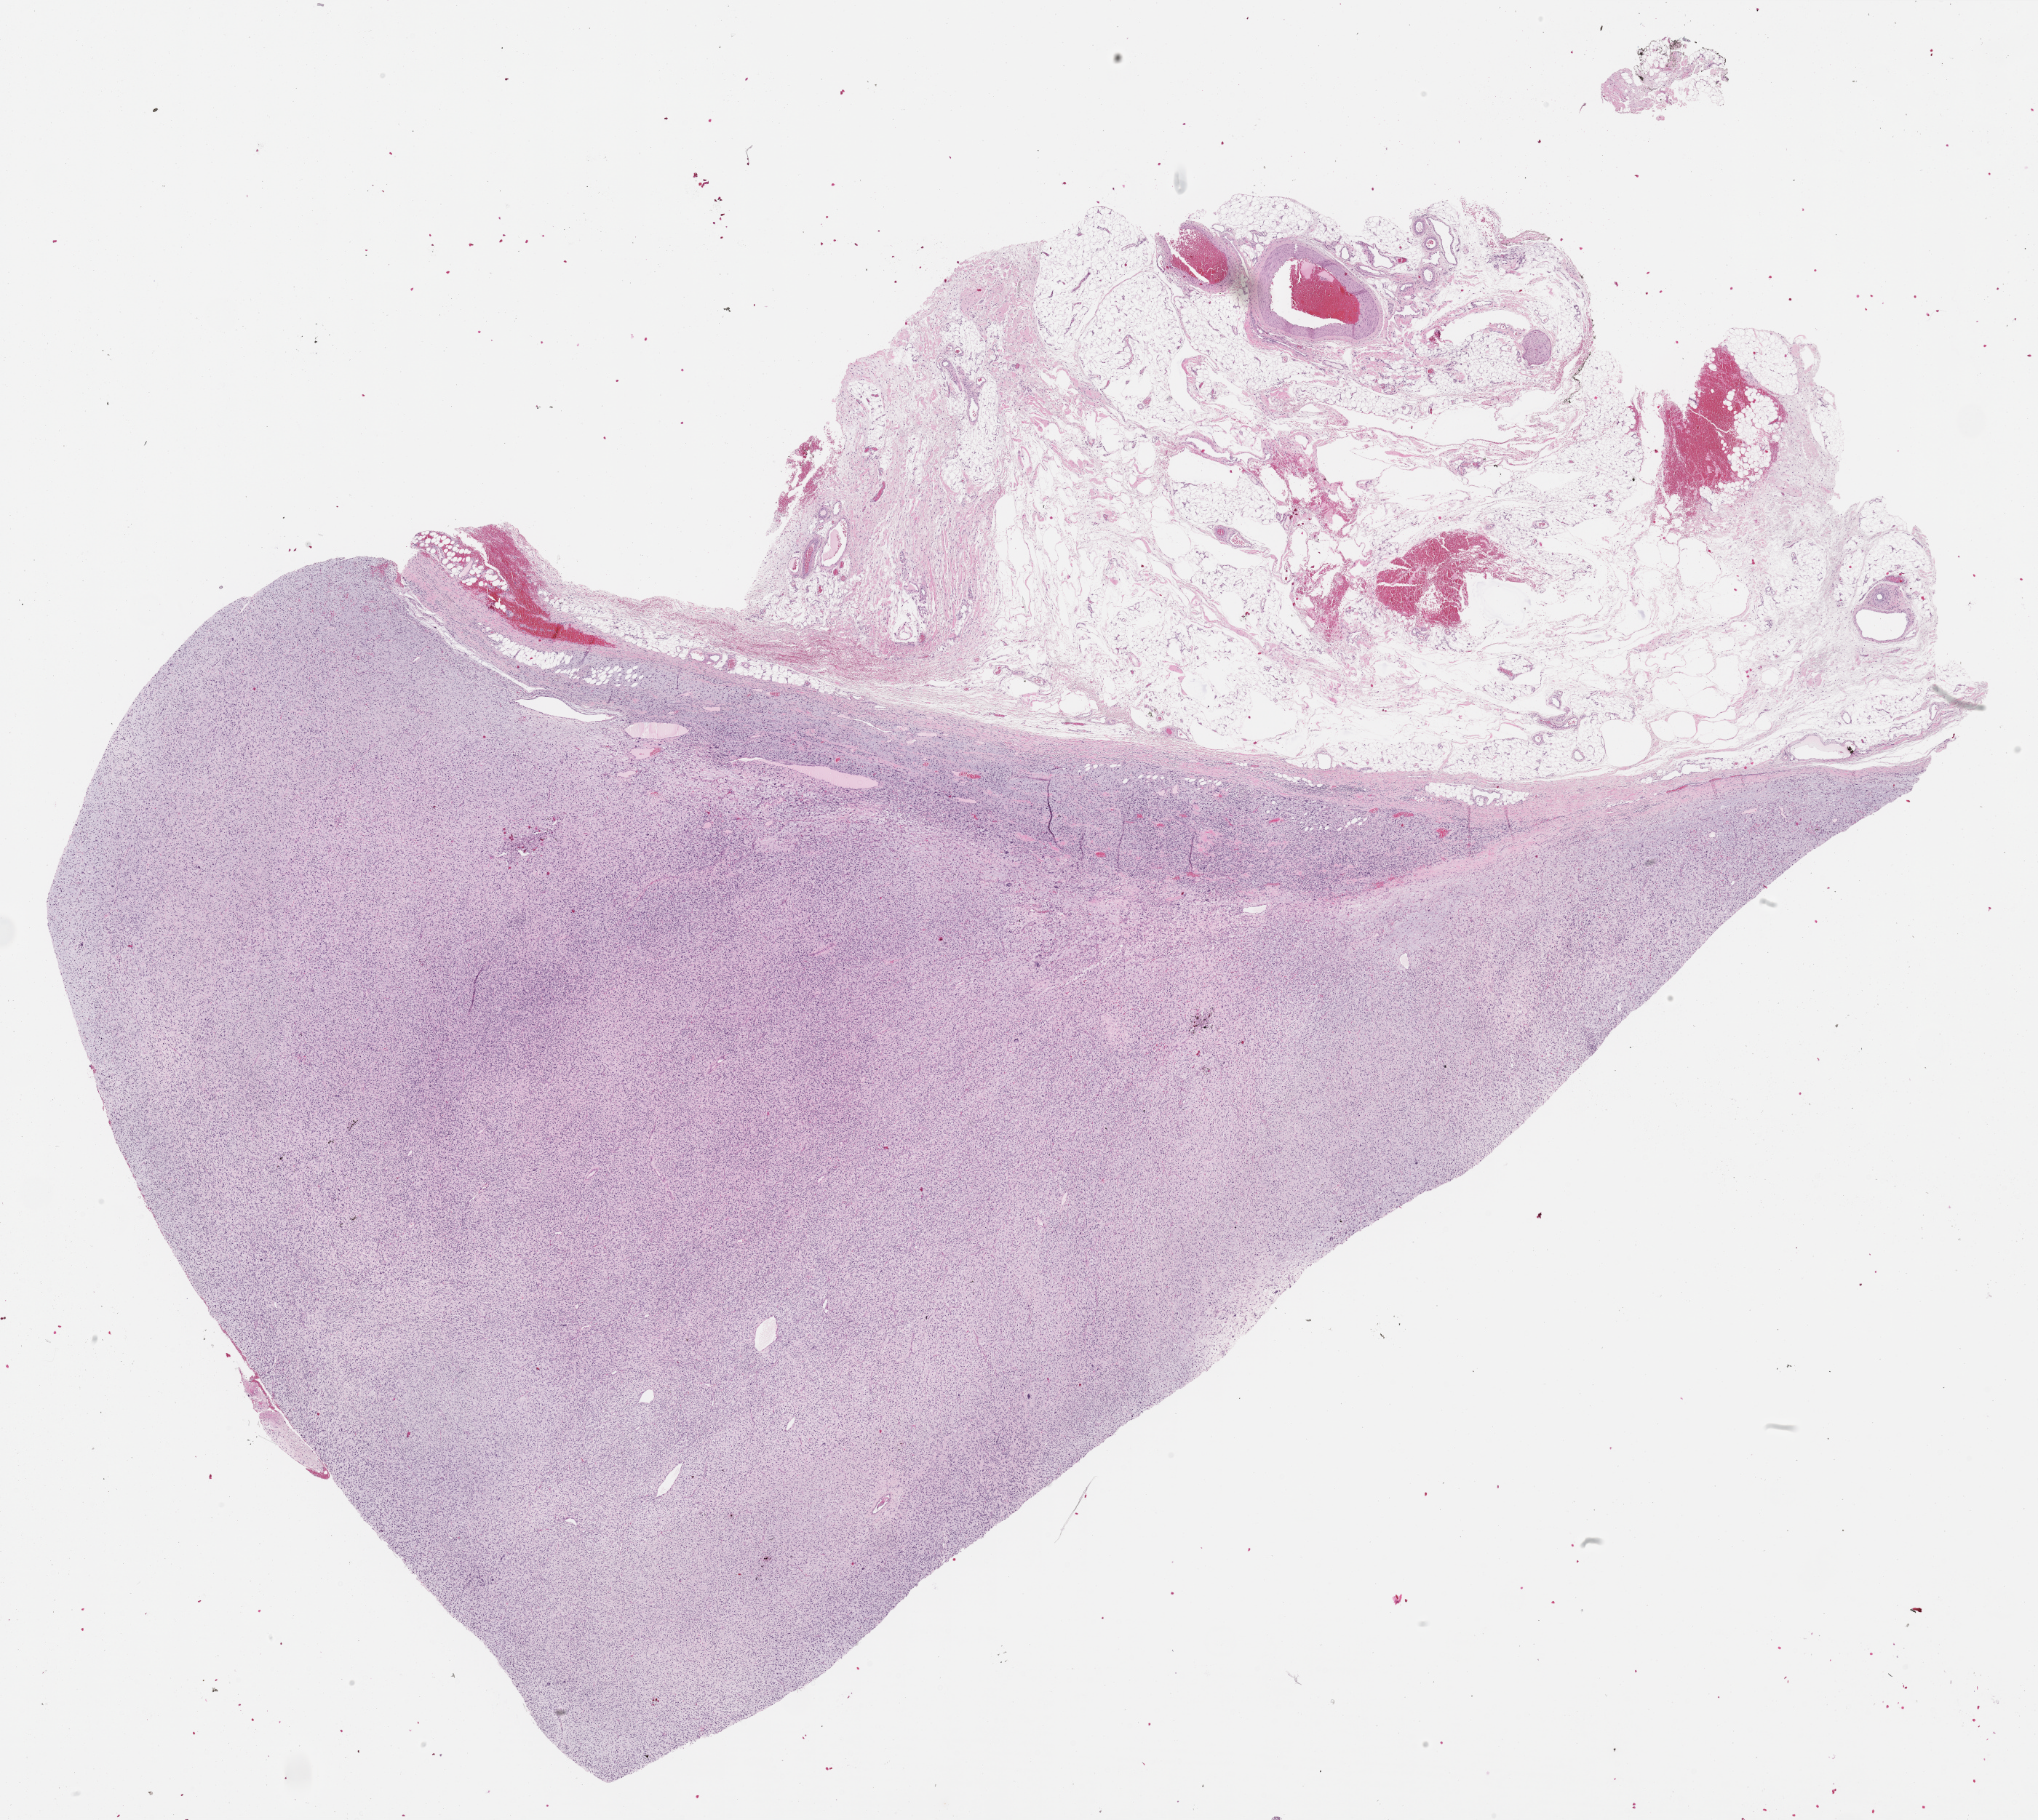
Digitized H&E tissue section (whole slide) — a low-resolution overview of the entire scanned area, about 22.7 x 20.2 mm (slide scanned at 40x); FFPE section; sample: primary tumour, connective, subcutaneous and other soft tissues. Female, age 50 years at initial diagnosis.
- diagnosis: Fibromyxosarcoma (connective, subcutaneous and other soft tissues of thorax)